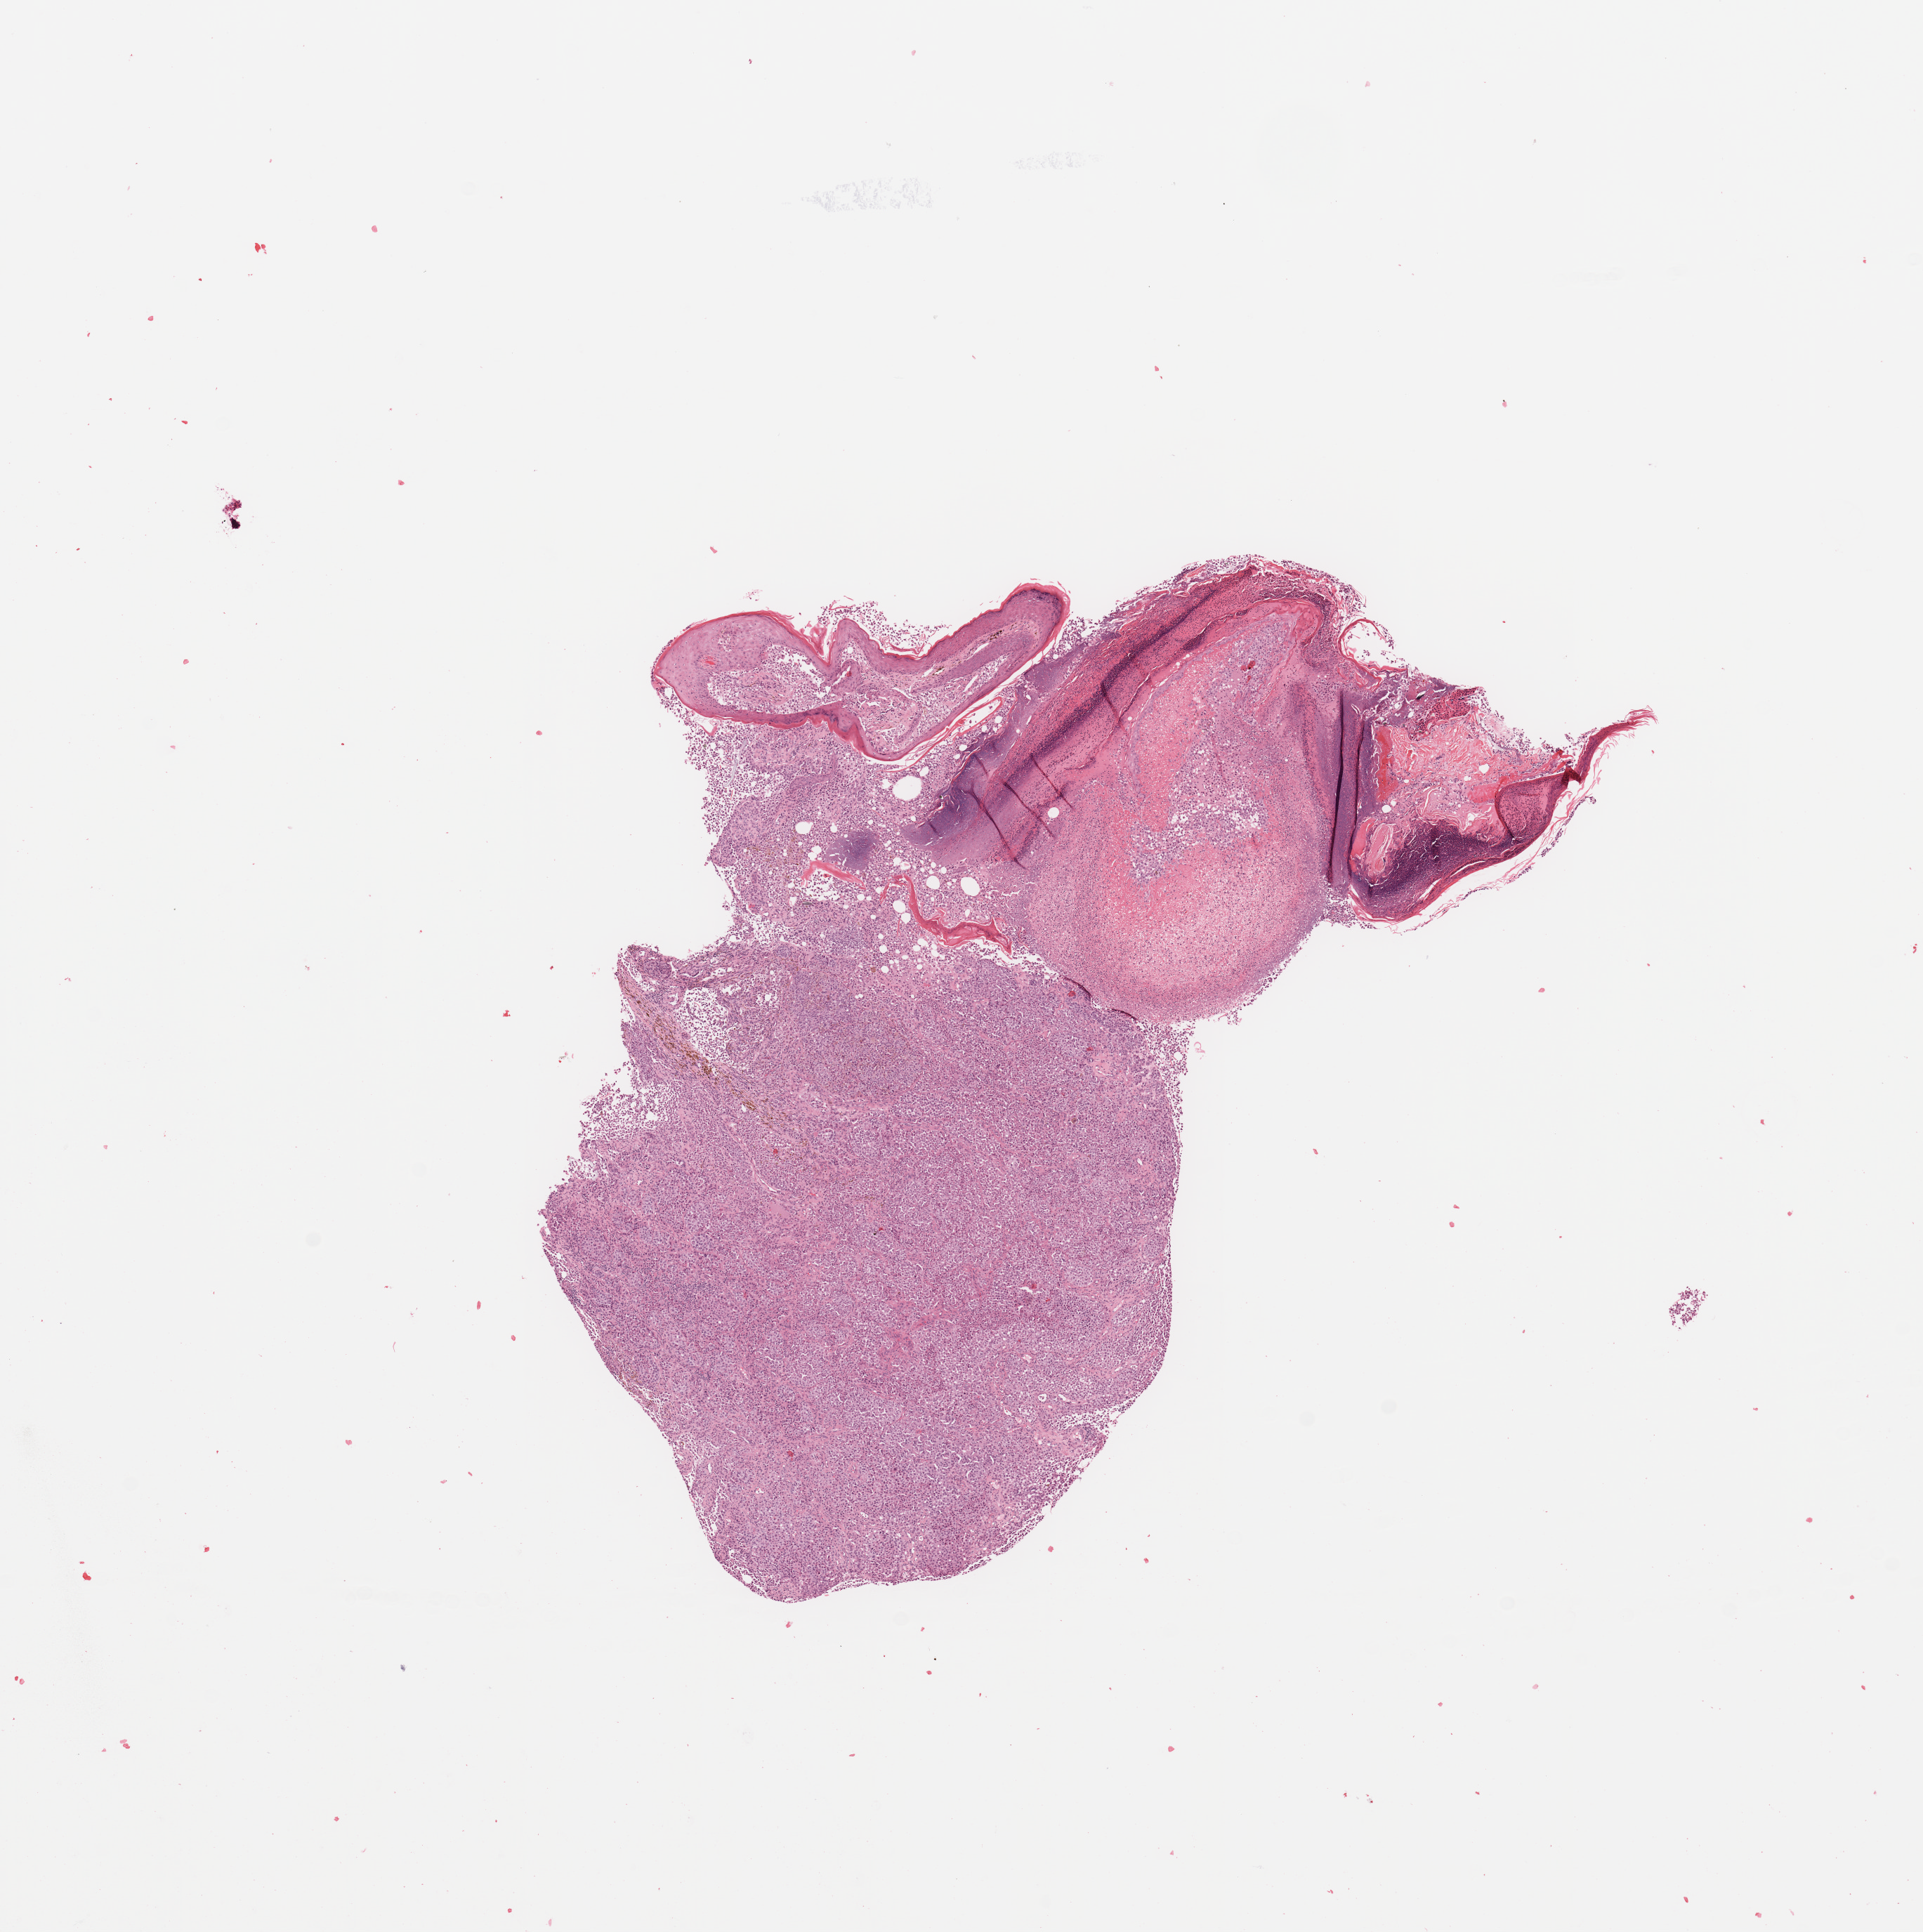
Whole-slide histology image, Hematoxylin and eosin (H&E) stained, whole scanned area (about 10.8 x 10.9 mm, slide scanned at 20x) shown as a low-resolution overview, melanoma tumour tissue; sampled site not recorded. 64-year-old female patient.
Histologic diagnosis: Malignant melanoma, NOS.